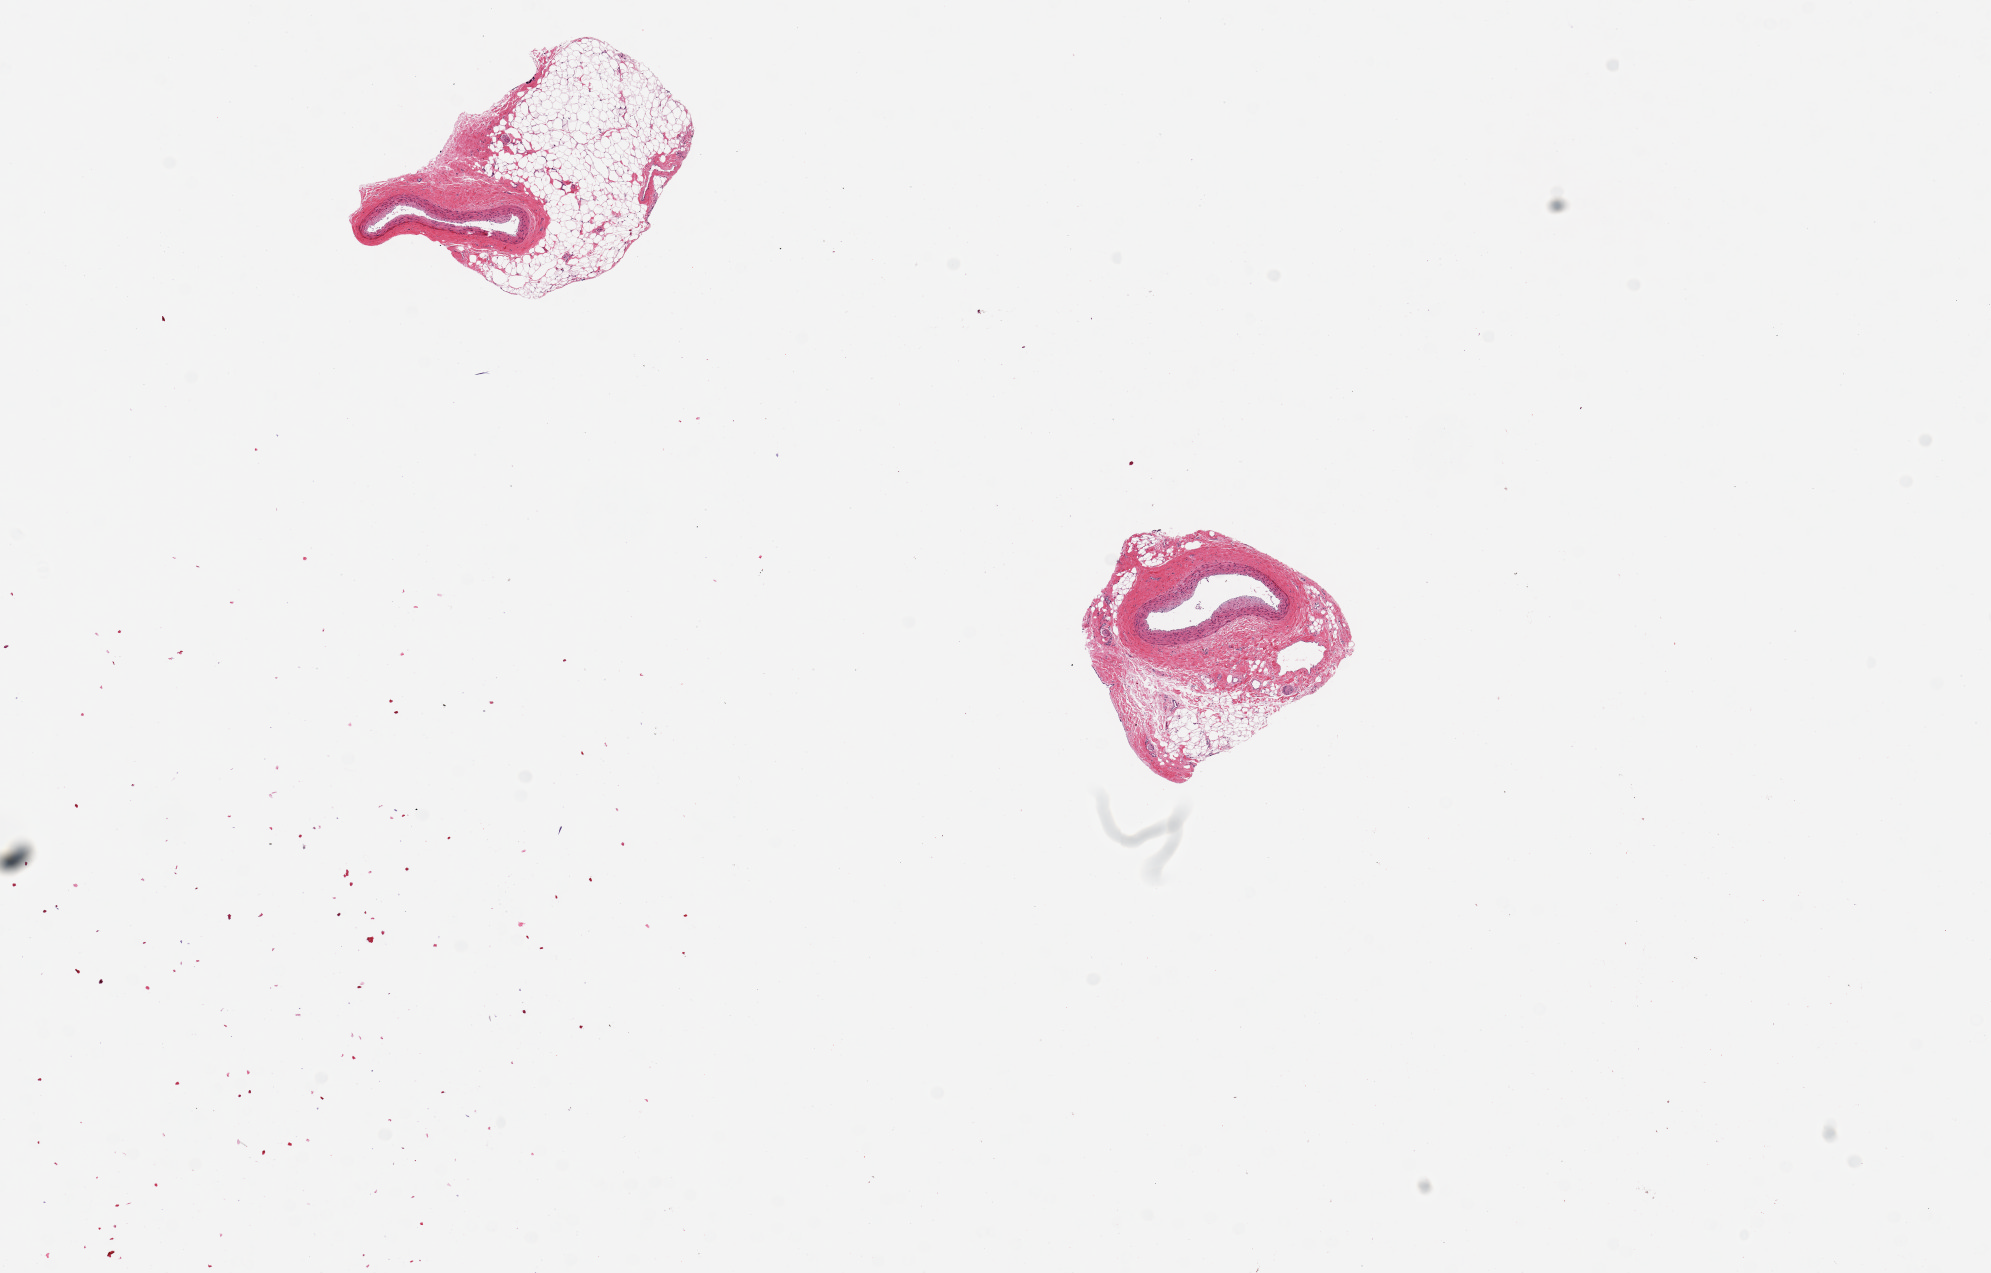
Digitized H&E-stained section — whole scanned area (about 15.8 x 10.1 mm, from a 20x scan) shown as a low-resolution overview, PAXgene-fixed paraffin-embedded (PFPE) section, sampled site (target tissue): coronary artery, donor tissue sample. Donor: male.
- pathologist's review note for this sample: 2 pieces ~1.5mm. Both with large adherent aggregates of fat ~1.5-2mm d